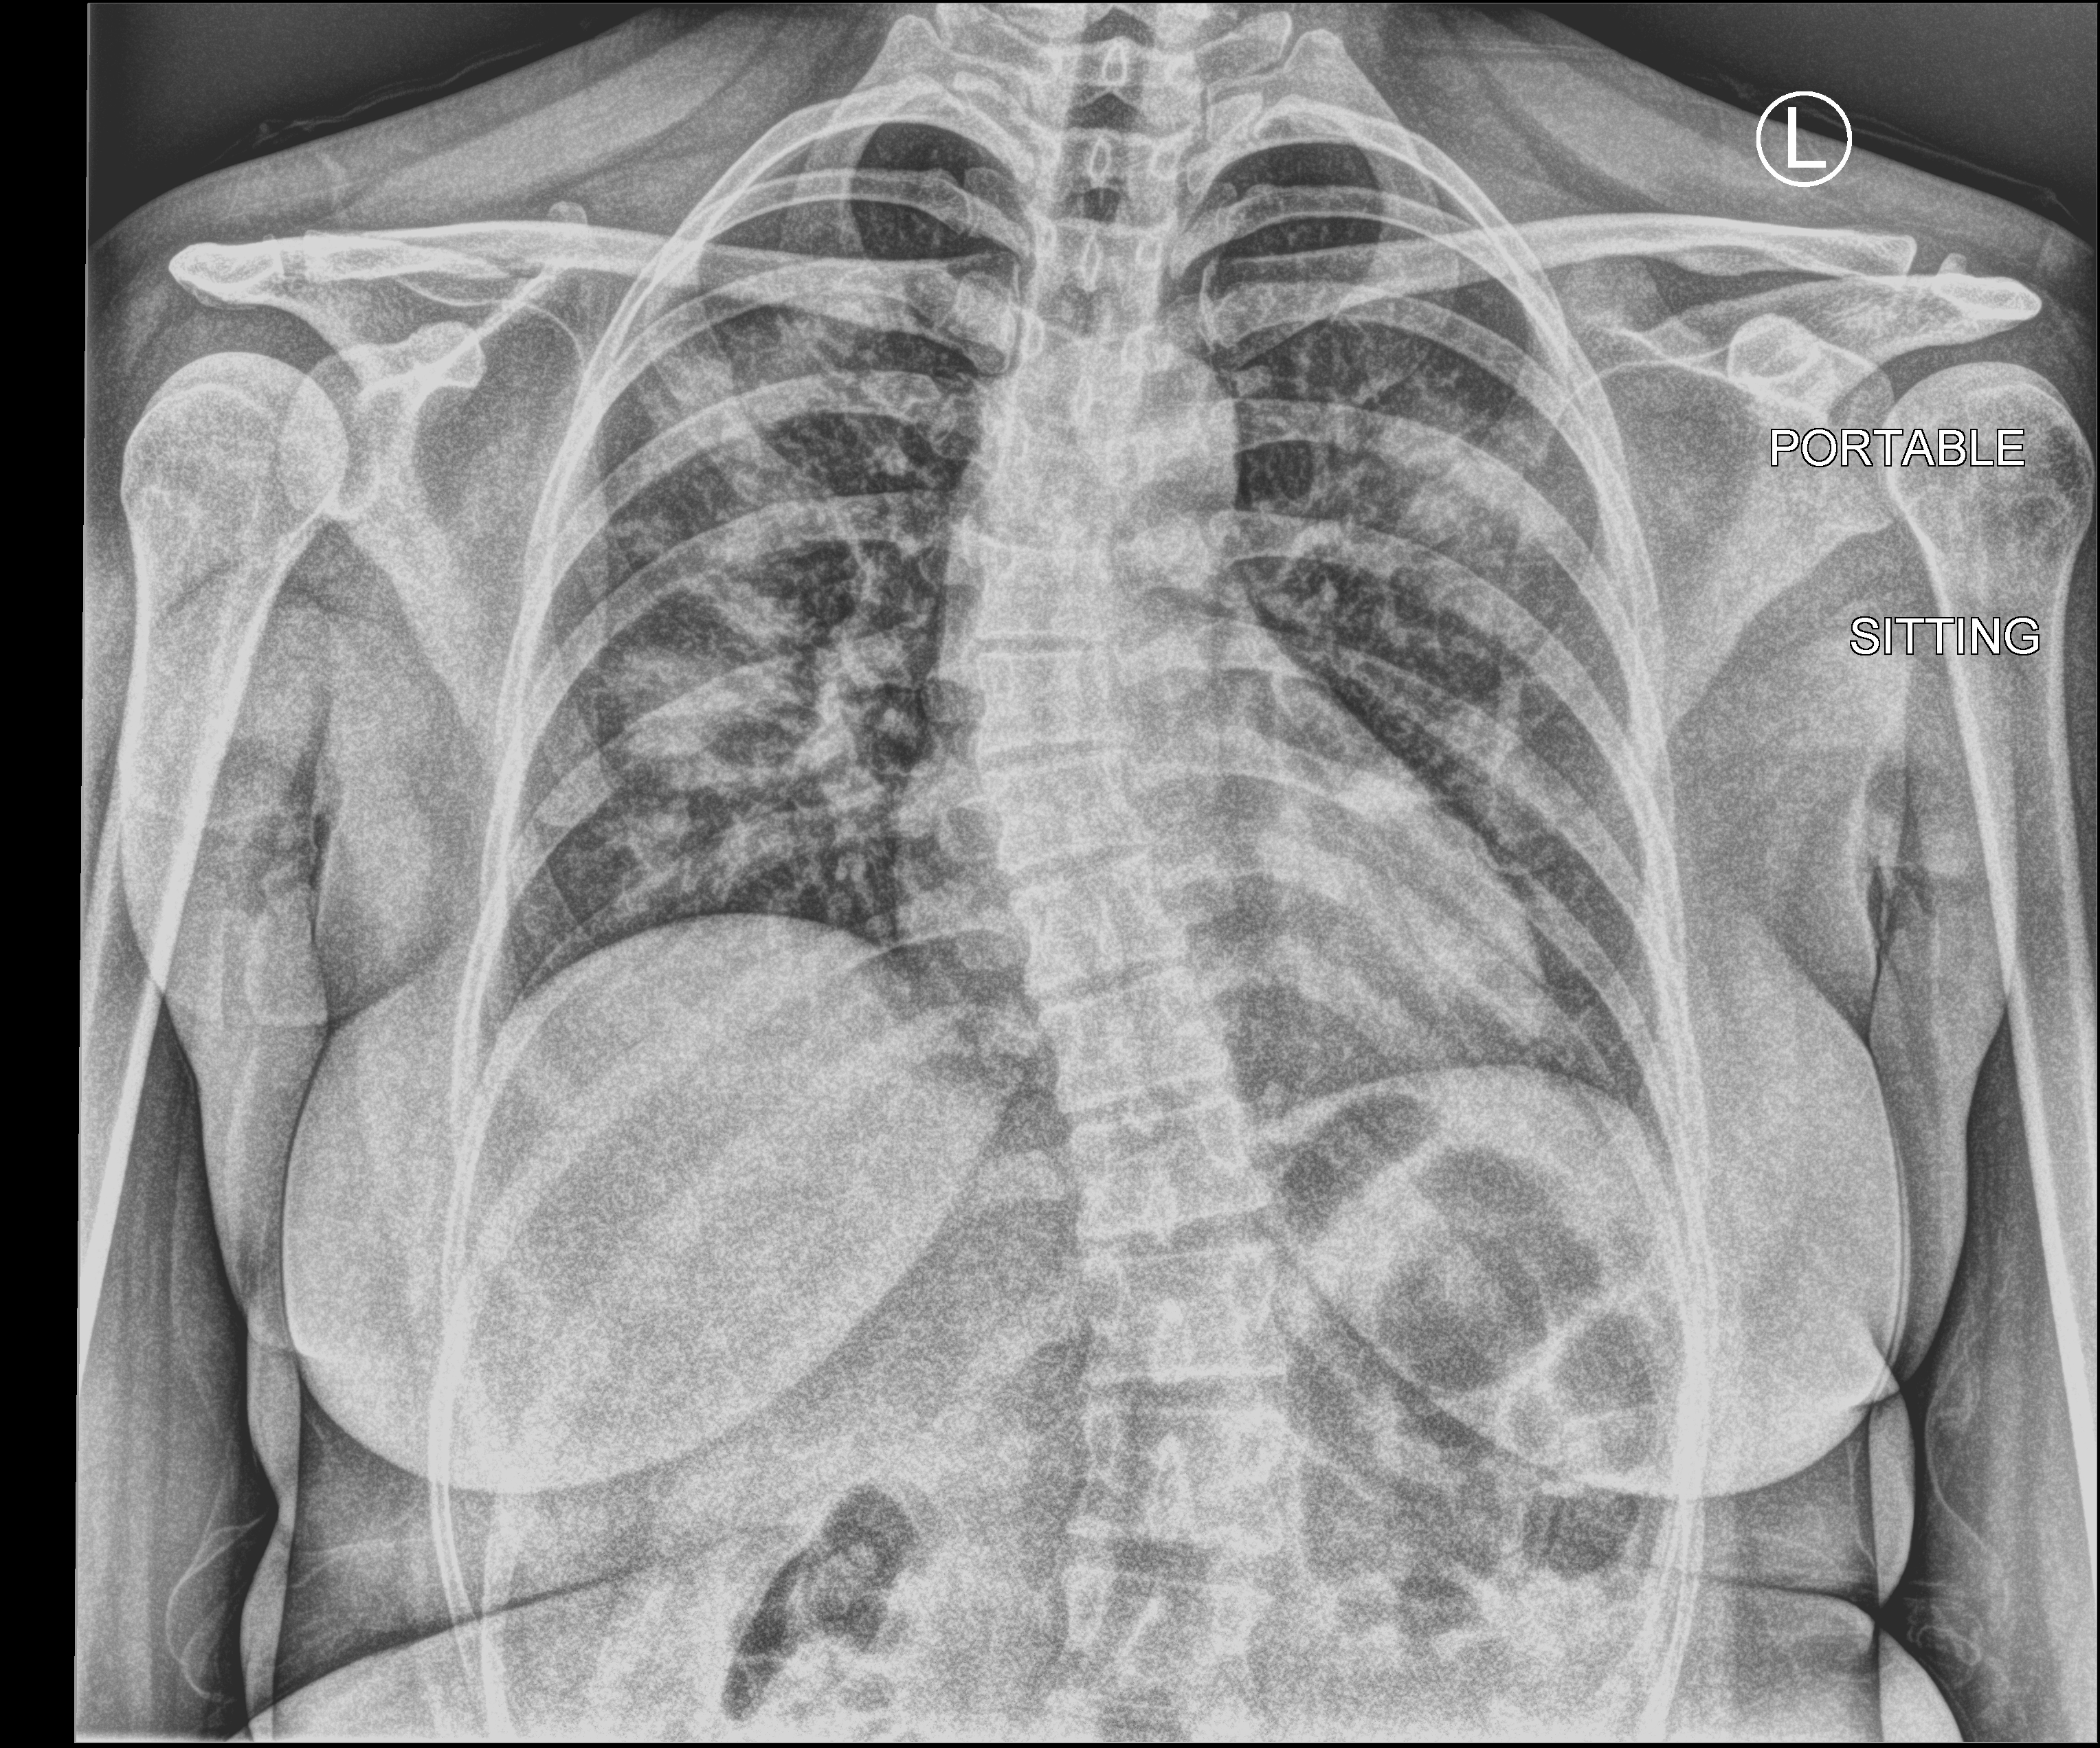
Portable chest radiograph, anteroposterior (AP) projection. Female patient hospitalised with COVID-19, age 18–59 years.
Hospital-stay facts (about this admission, not read from this image; timing relative to this image not recorded): admitted to intensive care during this hospital stay: no; length of hospital stay: 3 days.